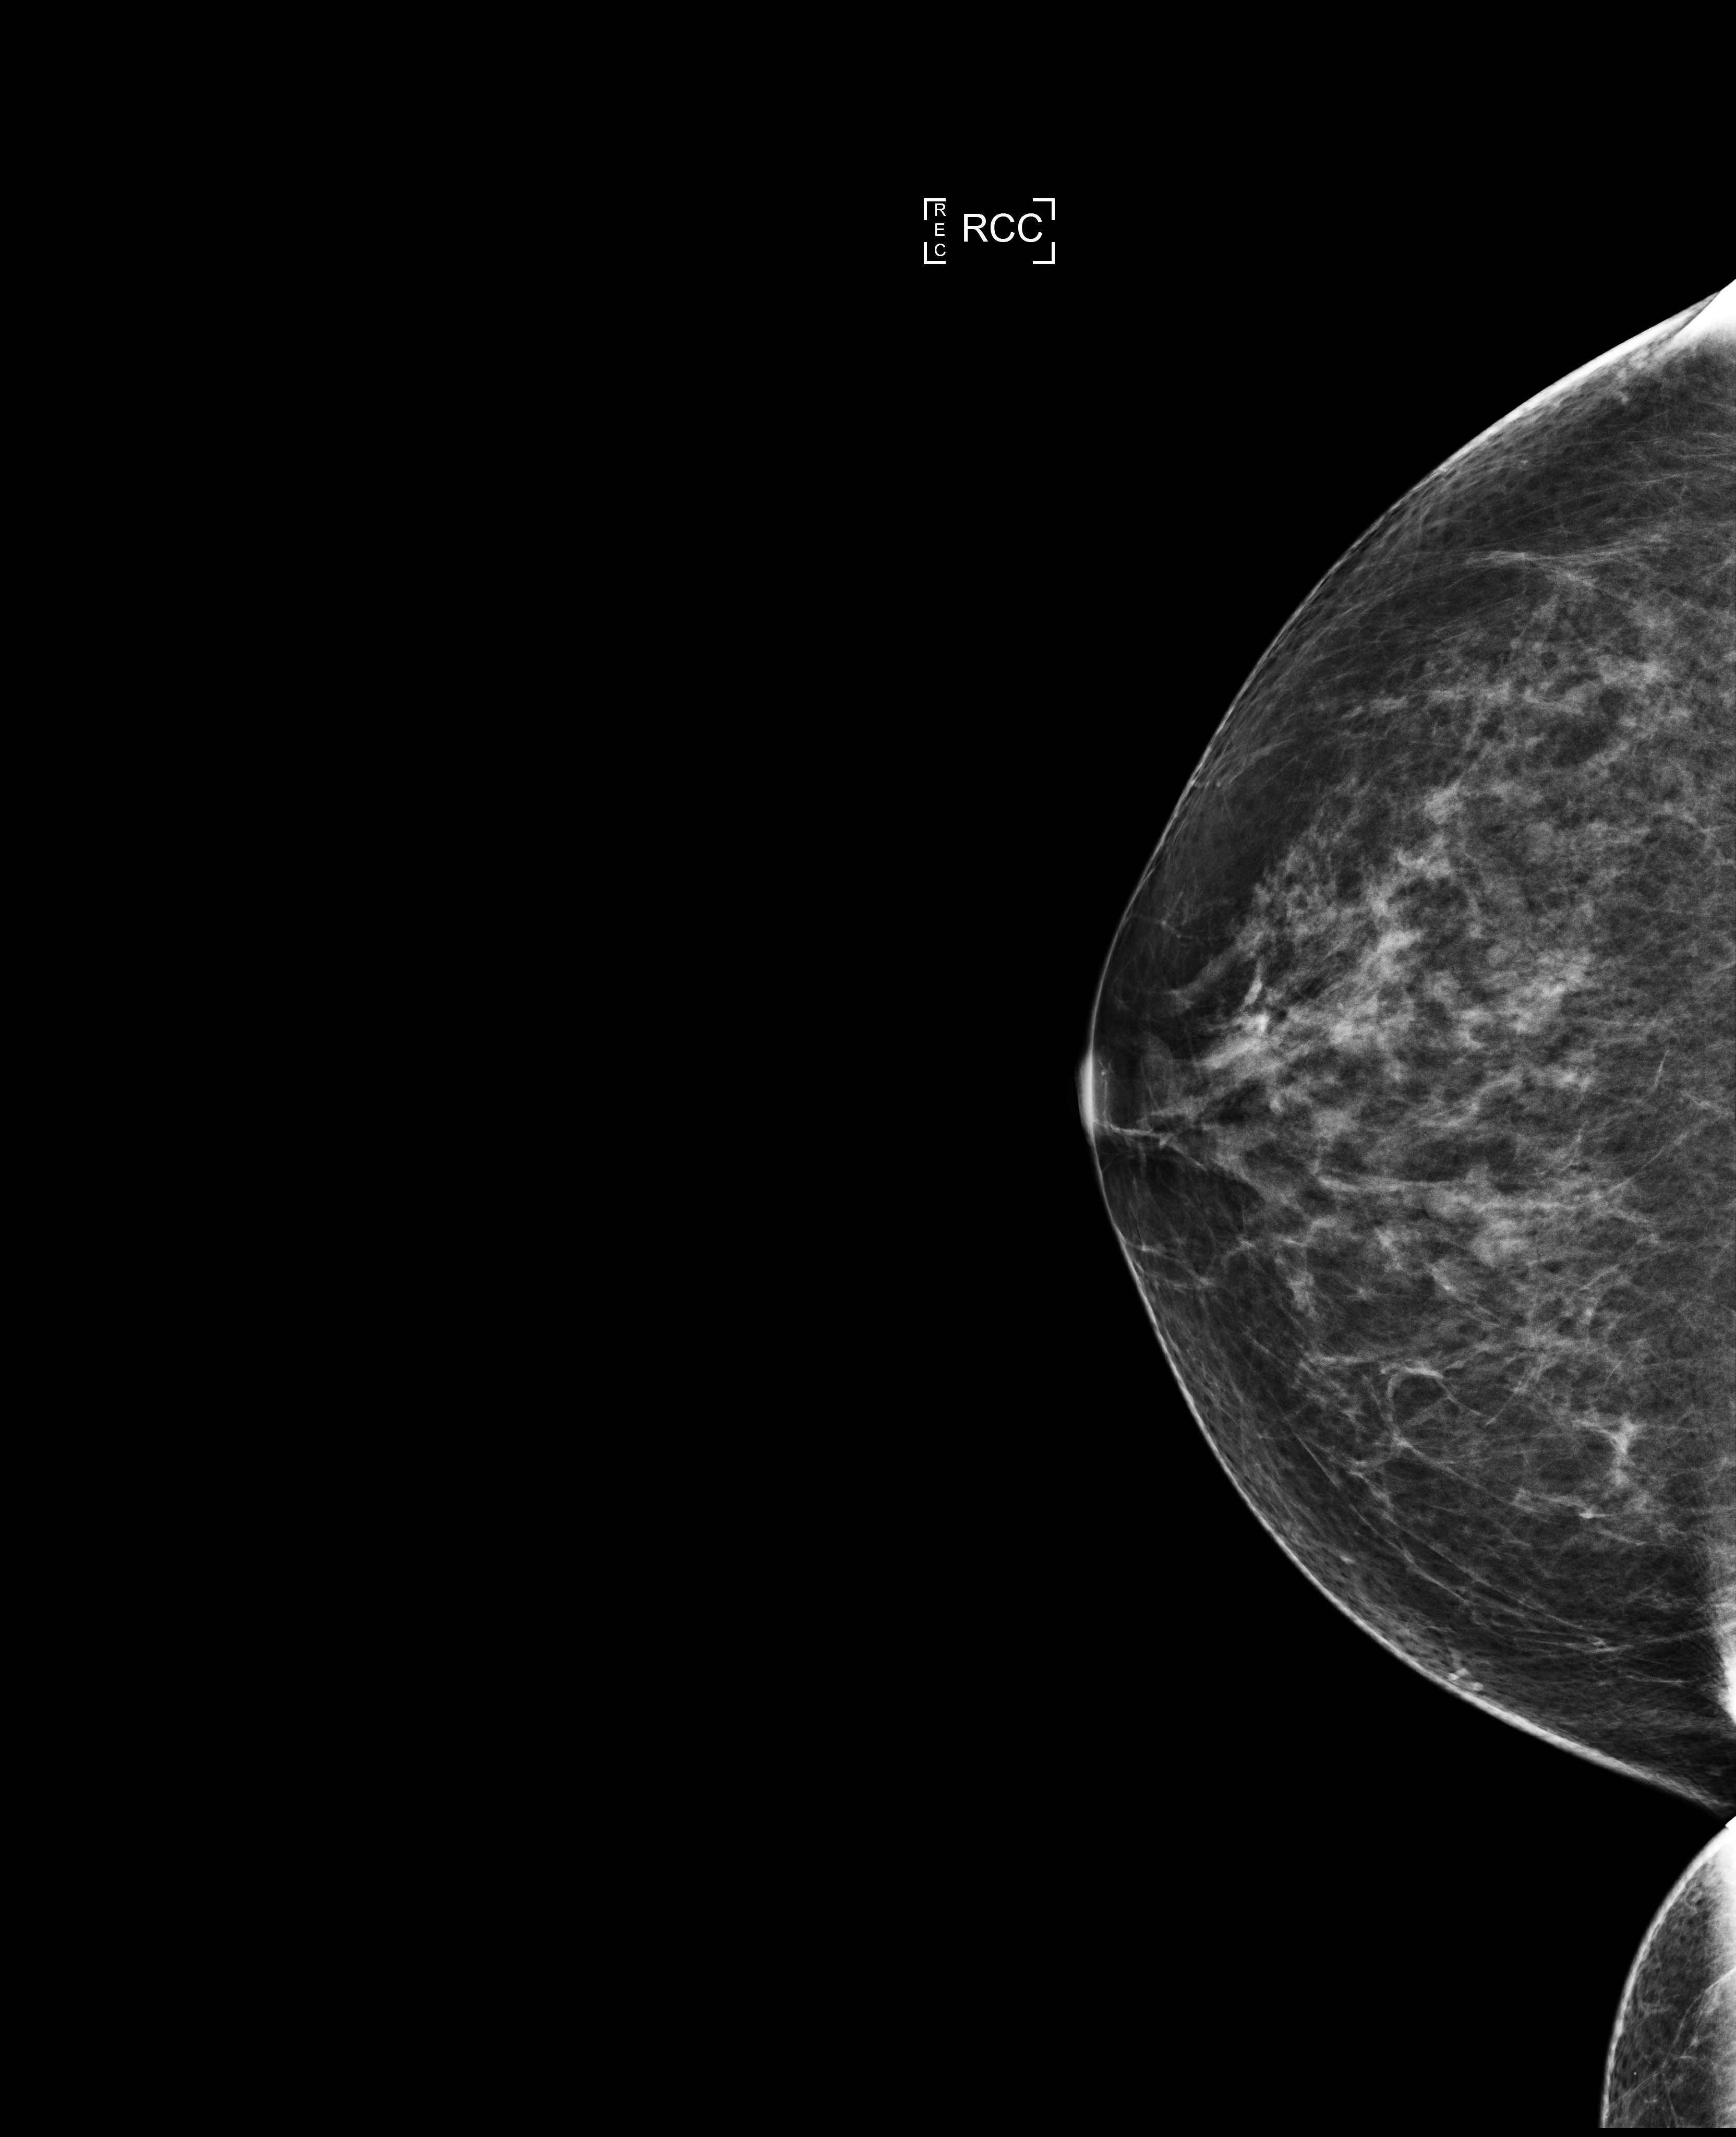
Screening examination. Patient: female, 53 years.
Image type: full-field digital mammogram. Breast: right. Projection: craniocaudal (CC) view.